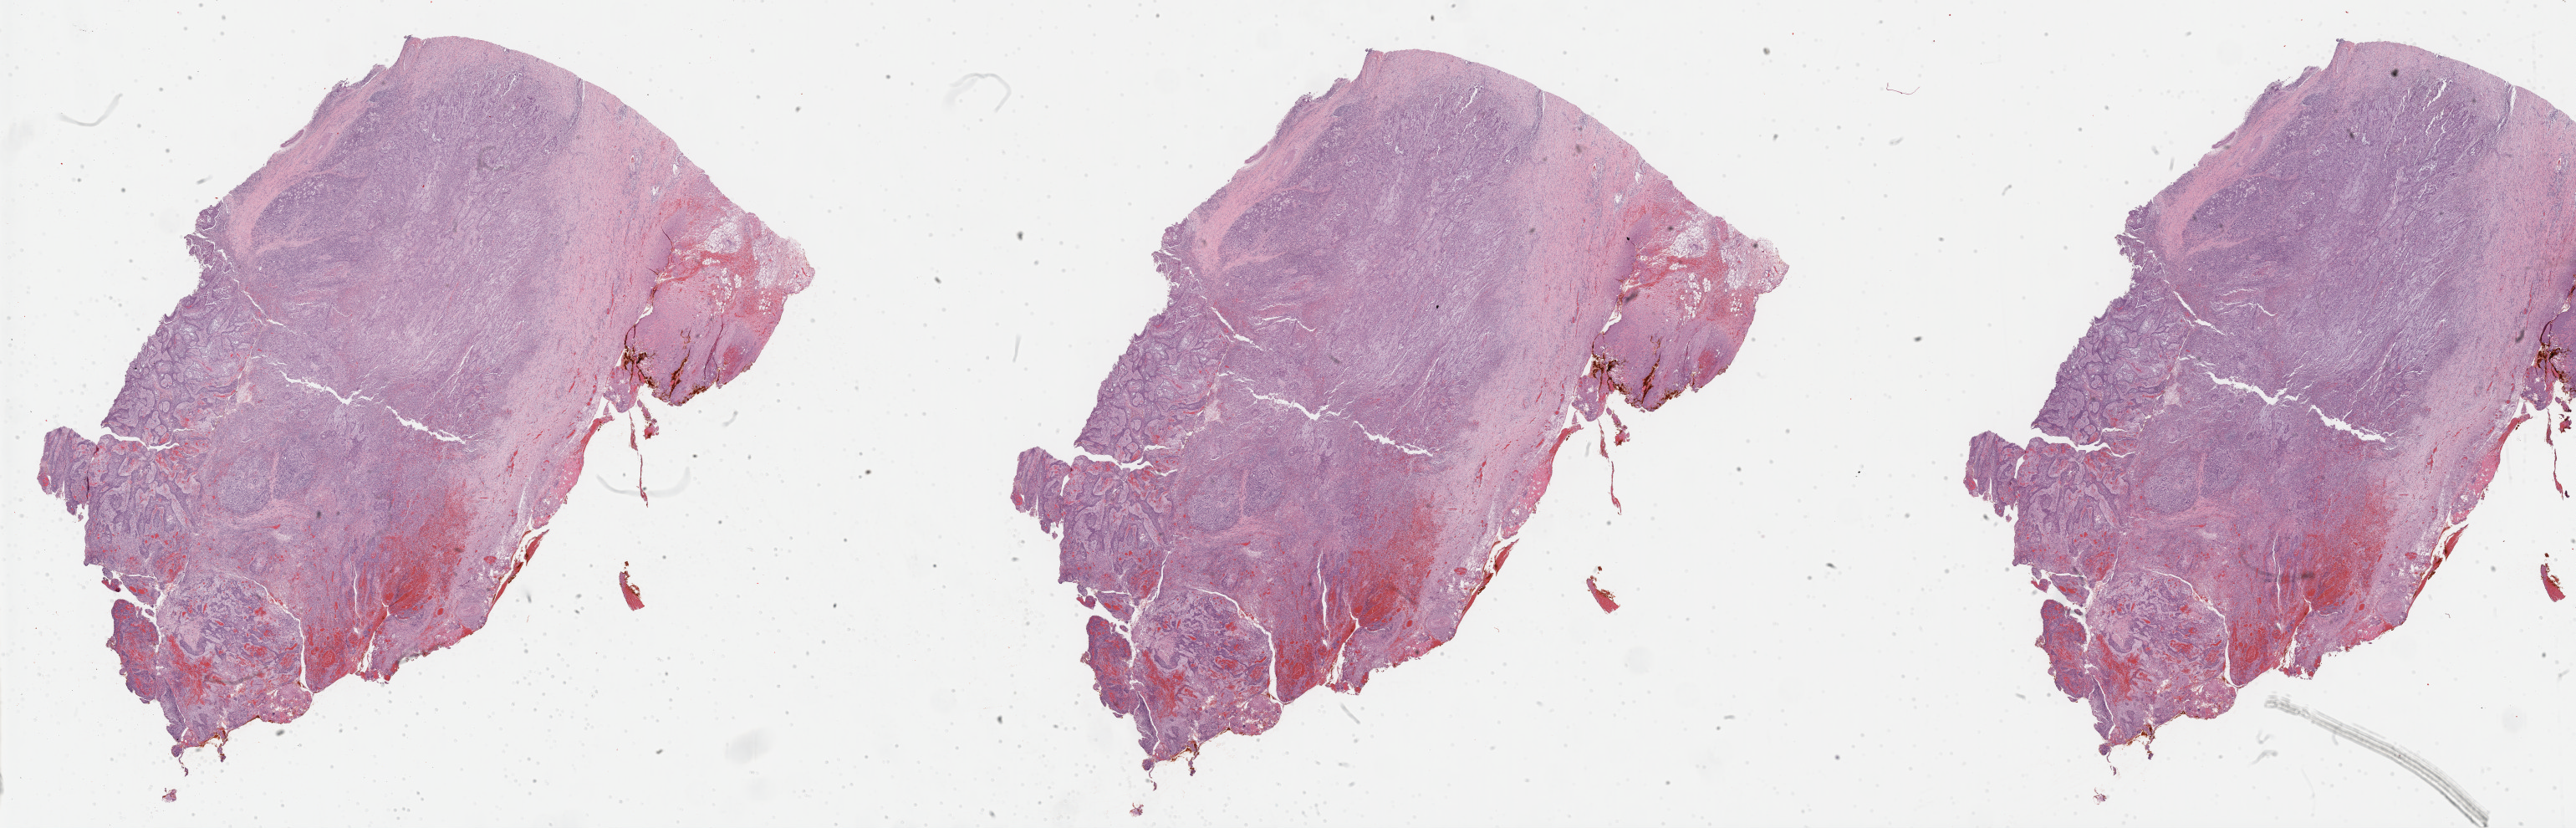
Digitized H&E tissue section (whole slide), shown as a low-resolution overview of the whole scanned area (about 49.8 x 16.0 mm, acquisition: 40x scan). Formalin-fixed paraffin-embedded (FFPE) diagnostic section. Head and neck, primary tumour sample. Female patient; age at initial diagnosis 61 years. Histologic grade: G2 (moderately differentiated).
Diagnosis: Squamous cell carcinoma, keratinizing, NOS (tongue, NOS). AJCC pathologic stage: III (7th edition).